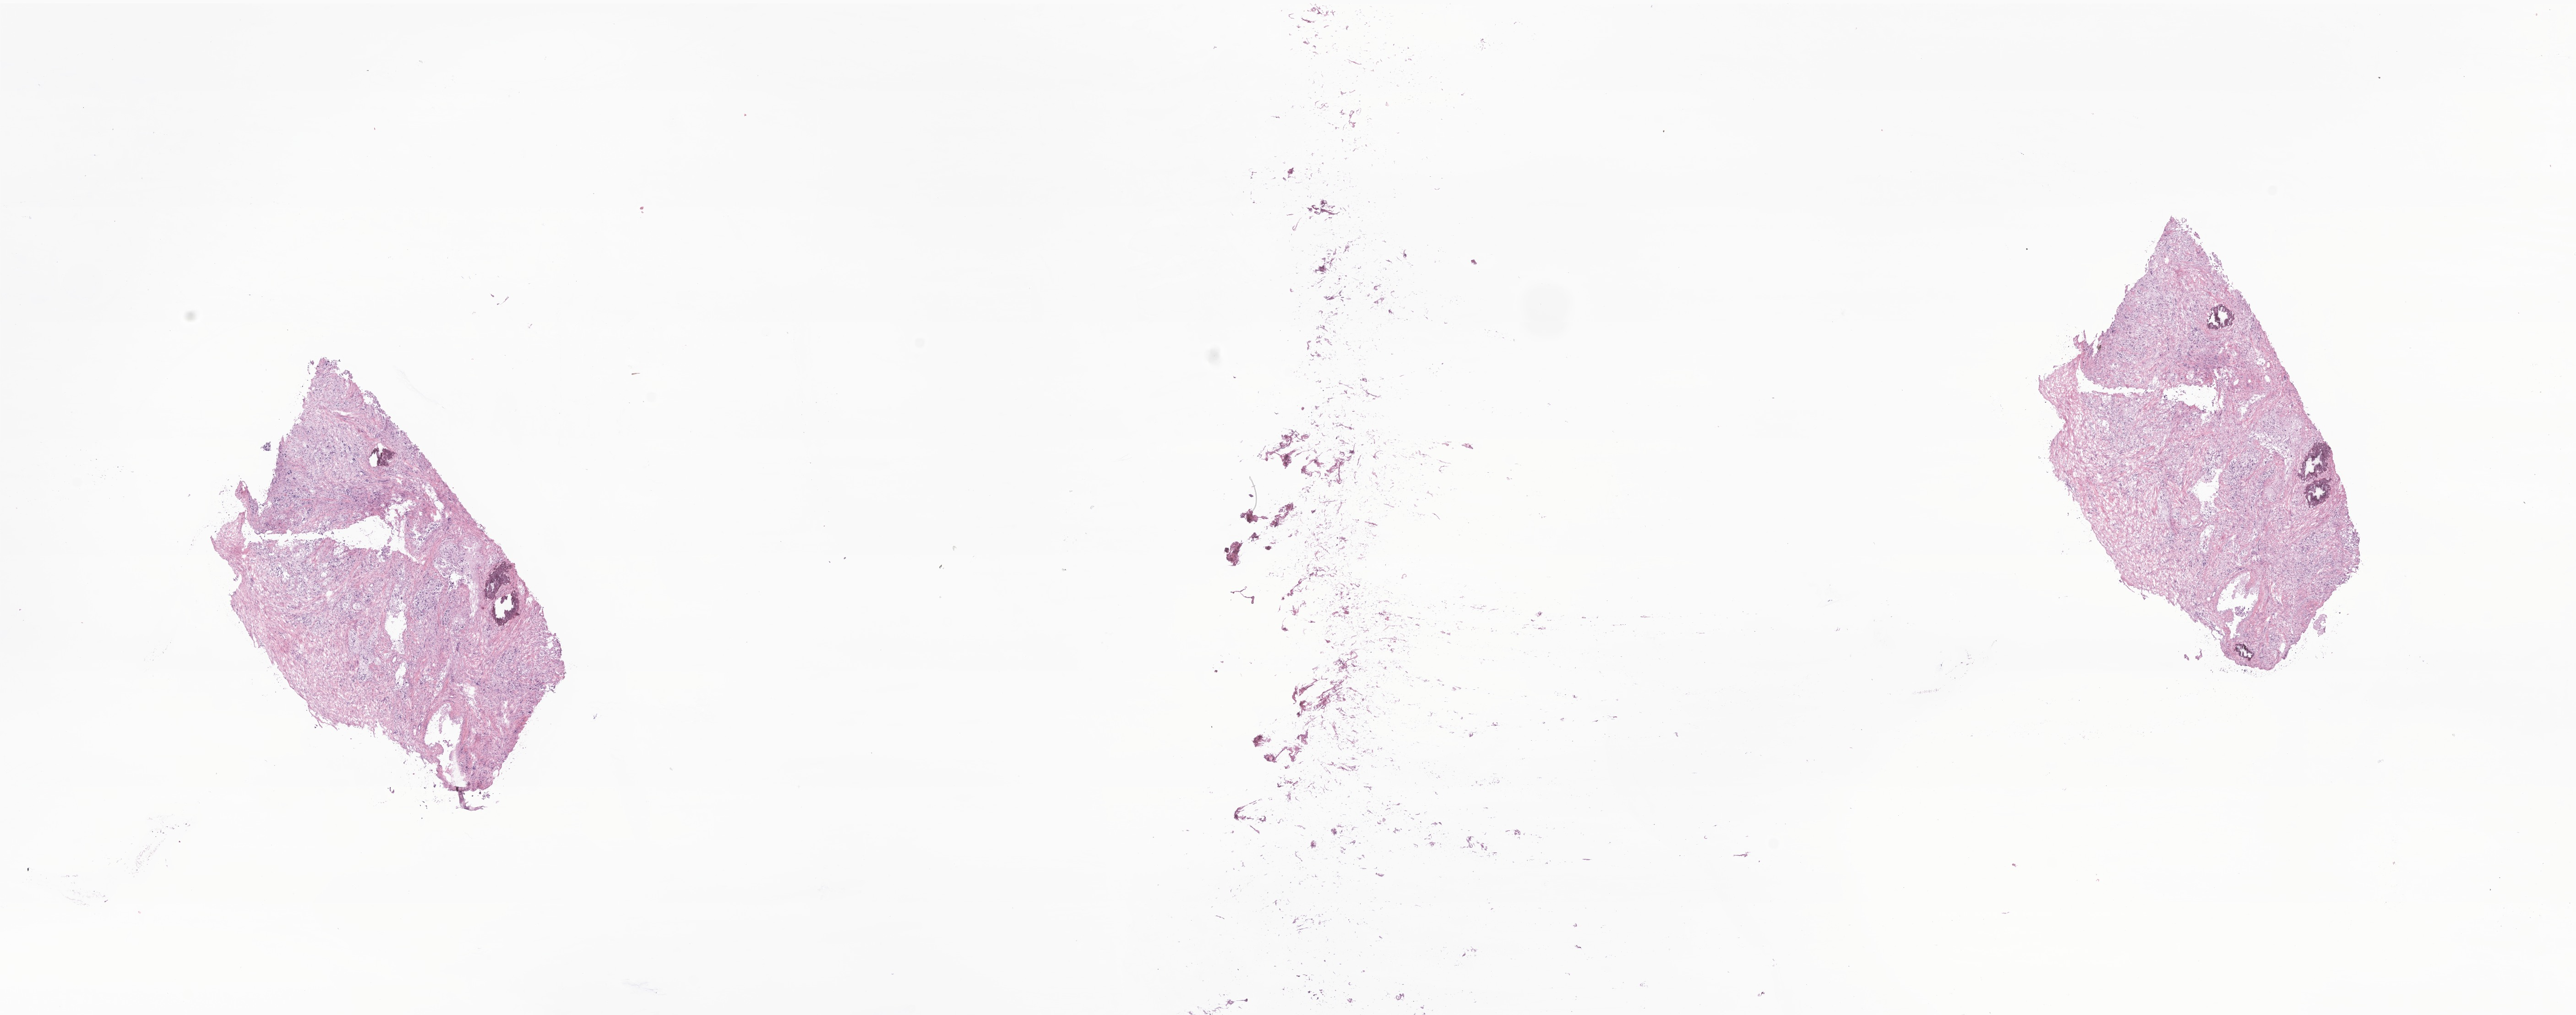
Whole-slide image, haematoxylin and eosin stain of tumor tissue from the adrenal gland, whole scanned area (about 23.7 x 9.3 mm) shown as a low-resolution overview, cryosection (OCT / tissue freezing medium). Male patient, age 862 days (about 2.4 years).
Diagnosis (ICD-O-3 morphology term): Neuroblastoma, NOS.